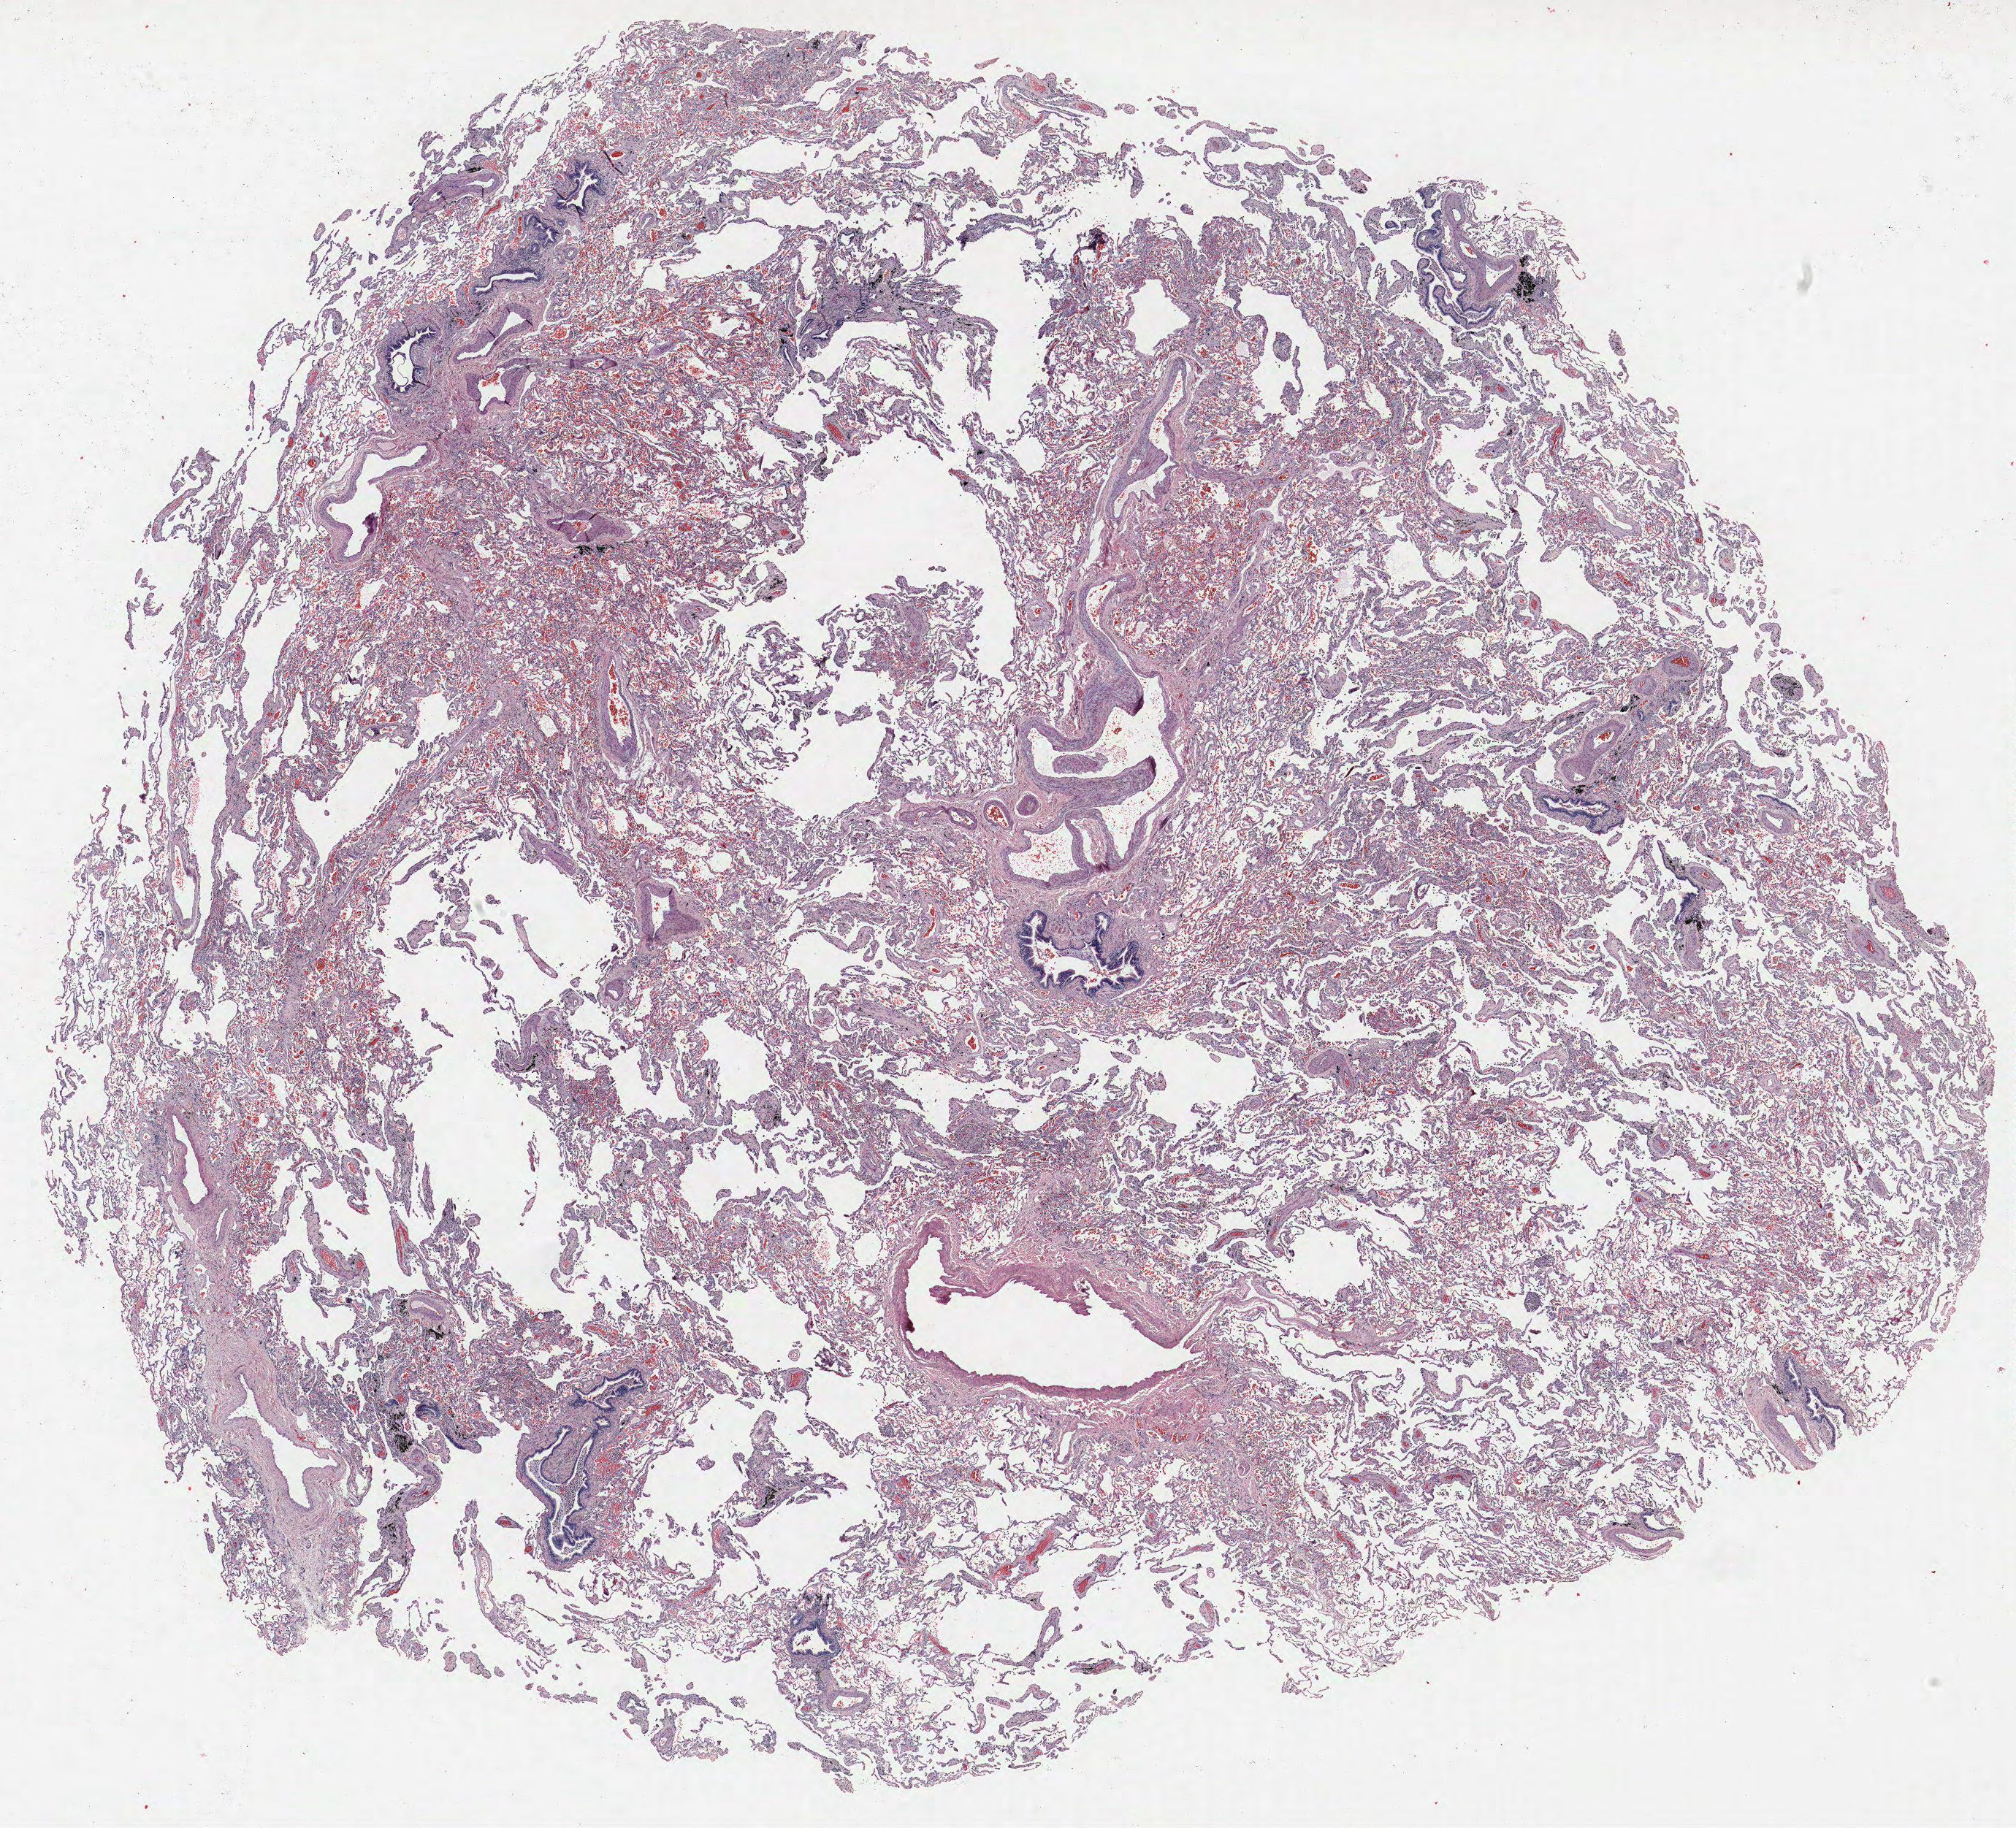
H&E-stained whole-slide image, whole scanned area (about 22.1 x 20.0 mm, acquisition: 40x scan) shown as a low-resolution overview, FFPE section, lung. Male patient, aged 68 at enrolment. Current smoker at enrolment. Grade: moderately differentiated (G2).
• primary tumour location (clinical record): right upper lobe
• participant's lung-cancer diagnosis: Squamous cell carcinoma, NOS
• tumour size (pathology): 7 mm
• stage (AJCC 6th edition): IIIA